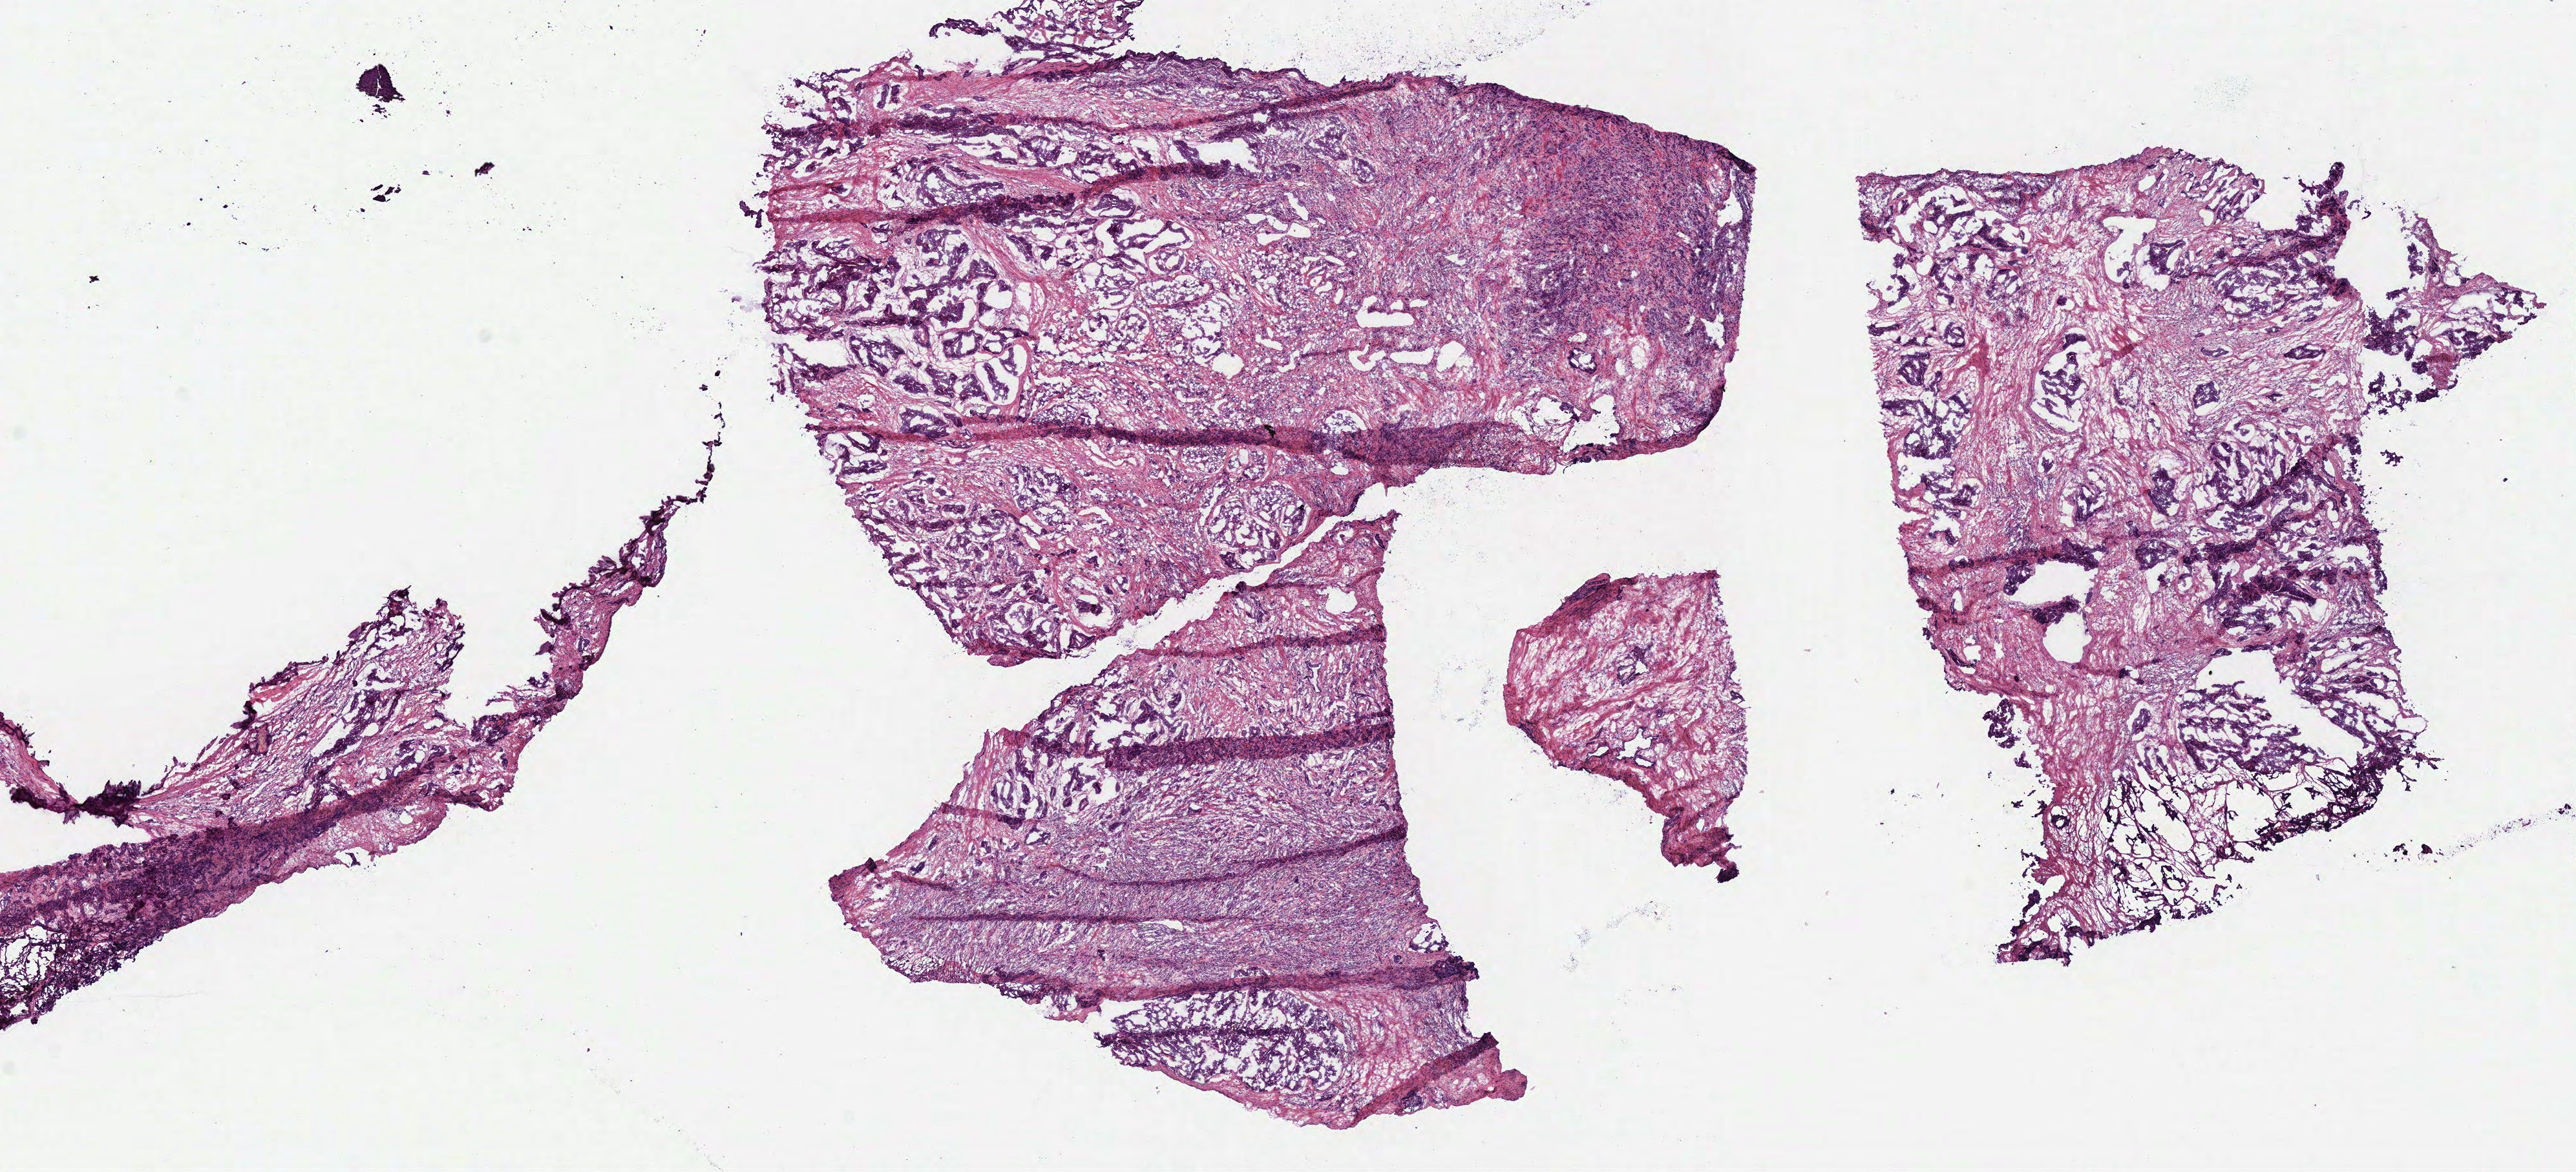
Whole-slide histology image, Hematoxylin and eosin (H&E) stained — whole scanned area (about 15.7 x 7.1 mm) shown as a low-resolution overview, frozen section from the bottom of the tissue portion, prostate, primary tumour sample. Patient: male, age at initial diagnosis 56 years. Gleason score: 9 (5+4). Composition of this section per pathologist review: tumour cells 80%, tumour nuclei 75%, normal cells 0%, stromal cells 20%, necrosis 0%.
- lymph nodes positive (case pathology): 0 of 7 examined
- pathologic diagnosis: Acinar cell carcinoma (prostate gland)